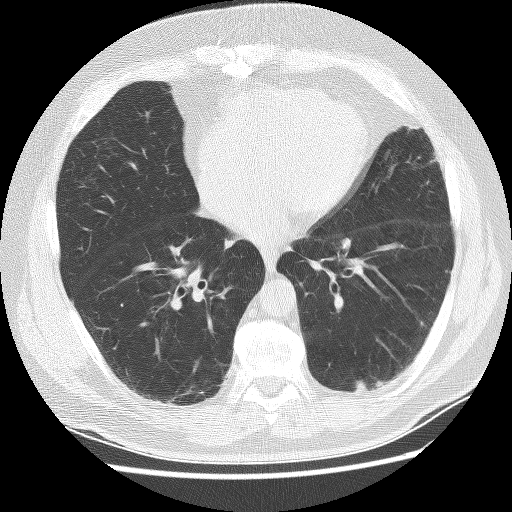
Chest CT (low-dose screening protocol), one axial image. Baseline screening round. Lung window (W 1500 / L -600 HU). 2.5 mm slice thickness. Lung (sharp) reconstruction kernel (BONE). 120 kVp. Slice 137 of 236 in the series. 512 × 512 image matrix. Male, age 65 years at enrolment. Former smoker at enrolment.
Expert reader's lesion annotation, bounding box (x1, y1, x2, y2) in pixels: (352, 370, 392, 405). Screening reader's record for this exam: no non-calcified nodule ≥4 mm recorded. Lung cancer was diagnosed 523 days after this screen (after the second annual screen): squamous cell carcinoma, NOS, left lower lobe, moderately differentiated (G2), stage IA (AJCC 6th edition), 20 mm at pathology.